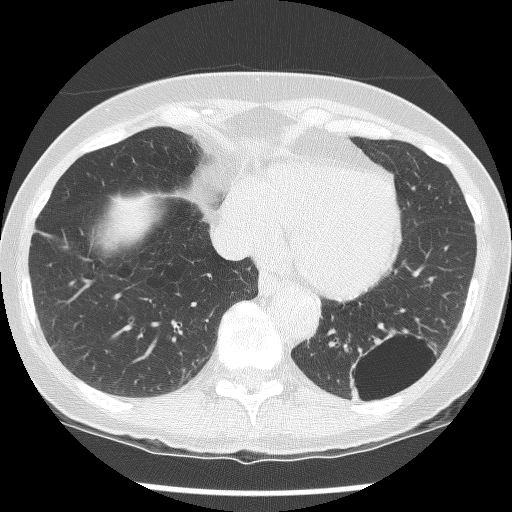
Low-dose screening chest CT, axial slice; second screening round (one year after baseline); lung window (W 1500 / L -600 HU); 2.5 mm slice thickness; lung (sharp) reconstruction kernel (BONE); 512 × 512 image matrix, field of view 300 × 300 mm. Female, age 61 years at enrolment.
Expert reader's lesion annotation, box from (x=330, y=321) to (x=437, y=415) px. The screening reader recorded 2 non-calcified nodules or masses ≥4 mm on this exam (left lower lobe, left lower lobe); which of them this box marks is not recorded.